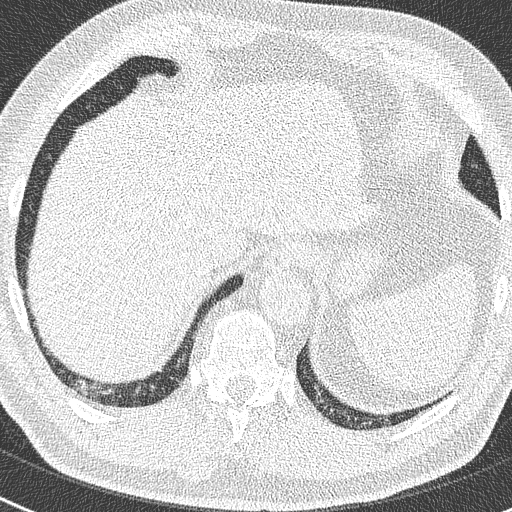
Low-dose screening chest CT, axial slice. Second annual screen. Lung window (W 1500 / L -600 HU). 512 × 512 image matrix. Male participant, aged 63 years at enrolment. Former smoker at enrolment.
- Expert-annotated lung lesion, bounding box <67,378,102,405> (left, top, right, bottom; pixels).
- No non-calcified nodule or mass ≥4 mm was recorded by the screening reader at this exam.
- Official screen result: negative screen, no significant abnormalities.
- Later outcome: lung cancer diagnosed 262 days after this screen — adenocarcinoma, NOS, right lower lobe, moderately differentiated (G2), stage IIIB (AJCC 6th edition), 17 mm at pathology.